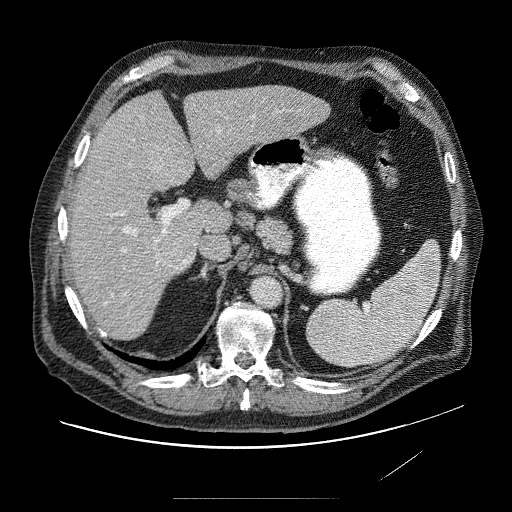
Contrast-enhanced abdominal CT (liver protocol), one axial slice; slice 48 of 89 in the series (ordered by position); 120 kVp; soft-tissue window (W 400 / L 40 HU); 2.5 mm slice thickness; 512 × 512 image matrix. From the clinical record (not read from this slice): diagnosis: hepatocellular carcinoma (patient treated with transarterial chemoembolisation; whether this scan precedes or follows treatment is not stated here); TNM stage (as recorded): Stage-IVA; Child-Pugh class: A; tumour differentiation: moderately differentiated; tumour nodularity: multinodular.
Structures marked on this image (semi-automatic segmentation, software-assisted and operator-edited):
- abdominal aorta: bounding box (x1, y1, x2, y2) in pixels: (251, 277, 281, 307)
- liver parenchyma outside the tumour (the mass and vessels are separate outlines, so this box may not span the whole liver): (64, 84, 334, 334)
- mass: (147, 136, 193, 262)
- liver vessels: (92, 117, 284, 313)